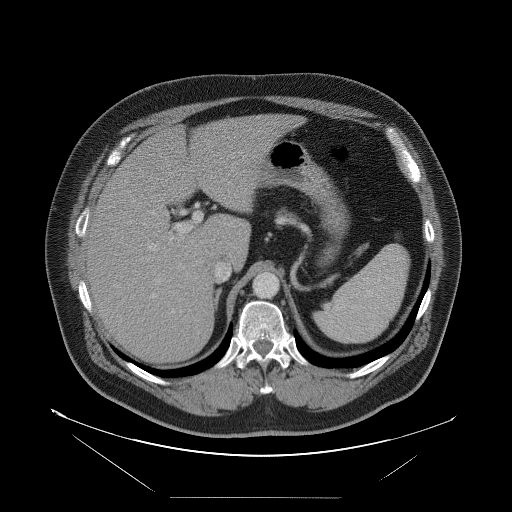
Contrast-enhanced abdominal CT, one axial slice; intravenous contrast given; soft-tissue window (W 400 / L 40 HU); 512 × 512 image matrix. Male patient, age 61 years. Case-level facts recorded for this patient, not image findings: diagnosis: colorectal cancer liver metastases, imaged before liver resection; multiple liver metastases: no; largest metastasis: 6.5 cm.
Structures marked on this image (manually delineated by an expert):
- hepatic veins: bounding box [x1, y1, x2, y2] px = [148, 244, 231, 283]
- liver: [88, 115, 291, 363]
- planned liver remnant (the part of the liver to remain after resection): [145, 115, 292, 260]
- portal vein (with intrahepatic branches): [151, 213, 202, 298]